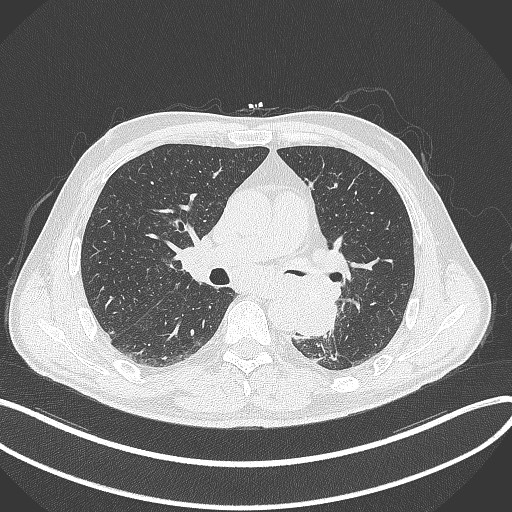
Chest CT, one axial slice; slice 194 of 329 in the series (ordered by position); reconstruction kernel B70f; 120 kVp; lung window (W 1500 / L -600 HU); 512 × 512 image matrix. Patient: male, 59 years. From the clinical record (not read from this slice): clinical TNM (as recorded): T2a N2 M0.
Structures marked on this image (bounding box drawn by a radiologist):
- lung tumour (recorded histology: squamous cell carcinoma): bounding box [x1, y1, x2, y2] px = [287, 282, 340, 338]